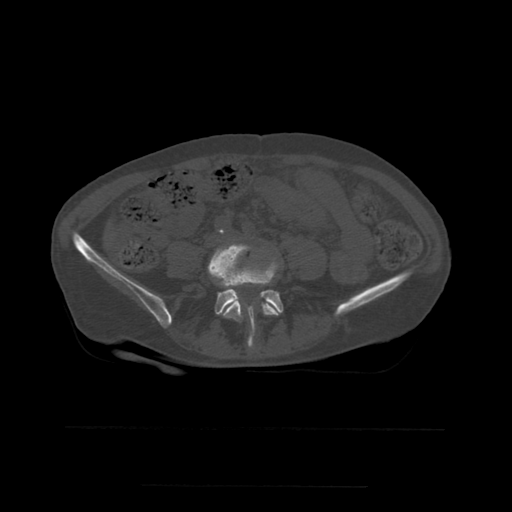
CT including the spine, one axial slice. Position 155 of 544 along the scan axis. Bone window (W 1800 / L 400 HU). 512 × 512 image matrix. Patient age 58 years. Case-level facts recorded for this patient, not image findings: primary cancer: lung.
Outlined on this slice (semi-automatically segmented with operator editing):
- L4 vertebra: bounding box (x1, y1, x2, y2) in pixels: (210, 244, 279, 348)
- L5 vertebra: (209, 260, 284, 327)